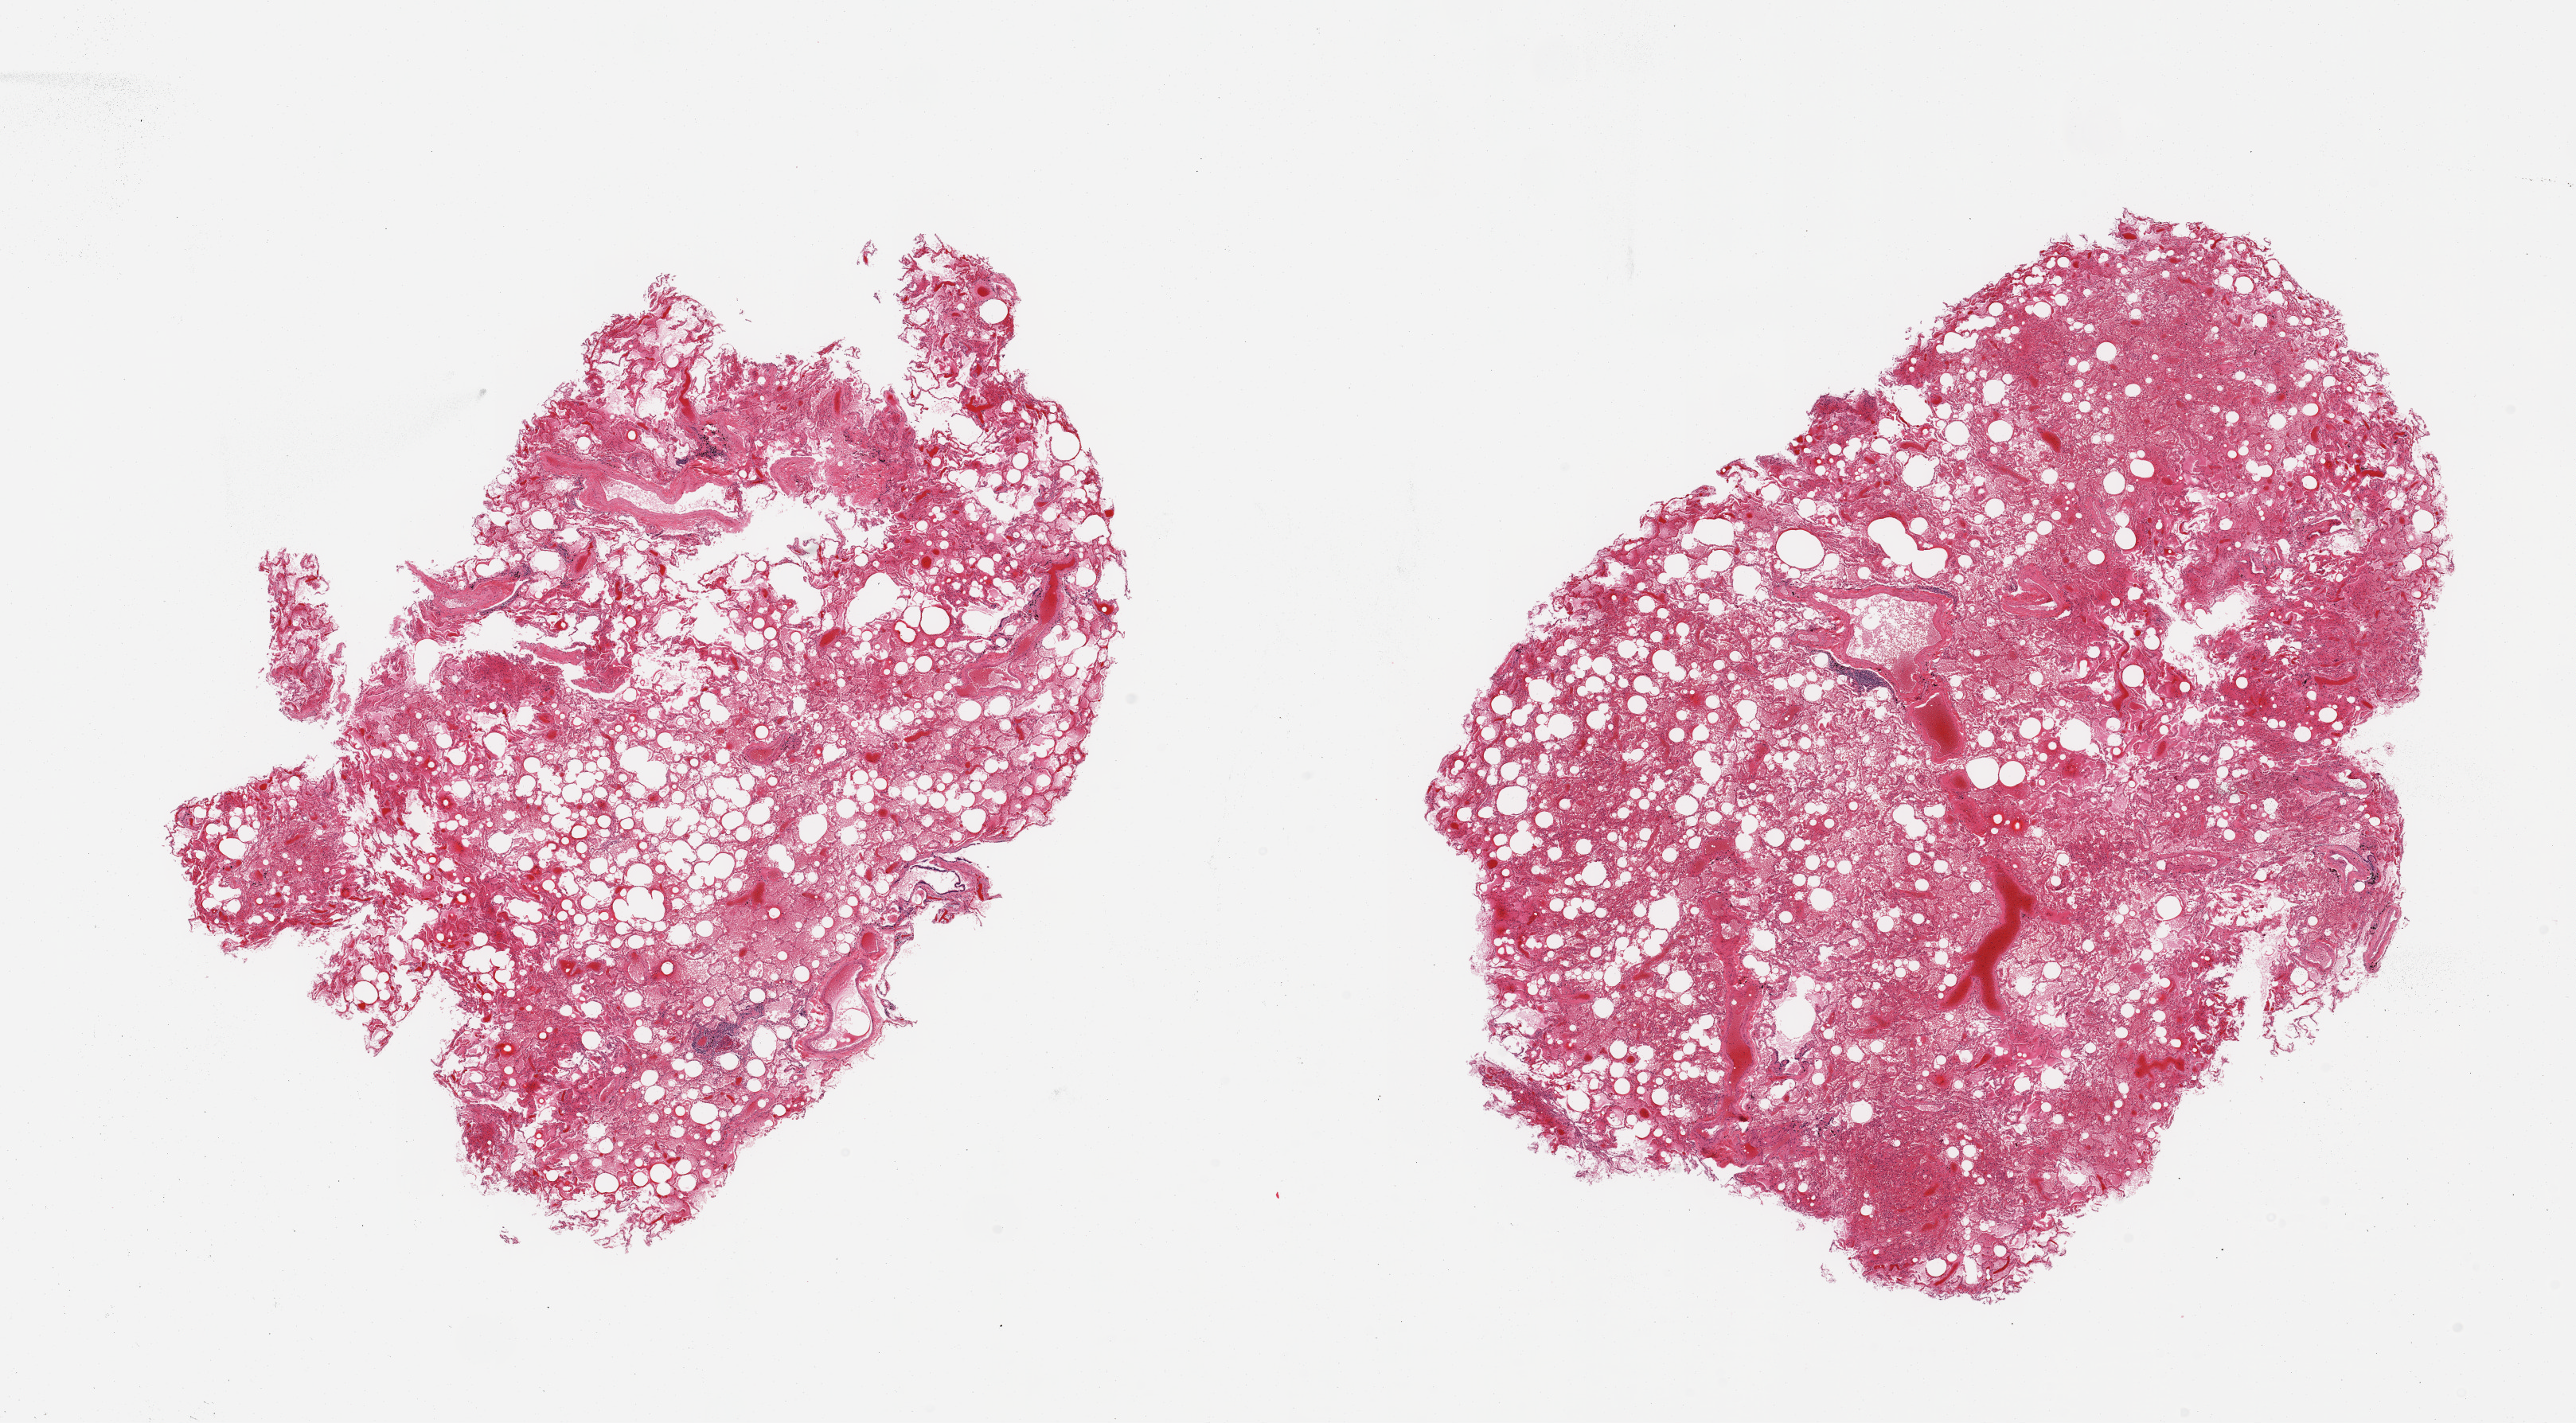
Digitized haematoxylin and eosin-stained section — low-resolution overview of the scanned area, about 25.6 x 14.1 mm; PAXgene-fixed, paraffin-embedded tissue; target tissue: lung; tissue donor sample. Donor: male.
* pathologist's review note for this sample: 2 pieces, moderate-severe alveolar congestion